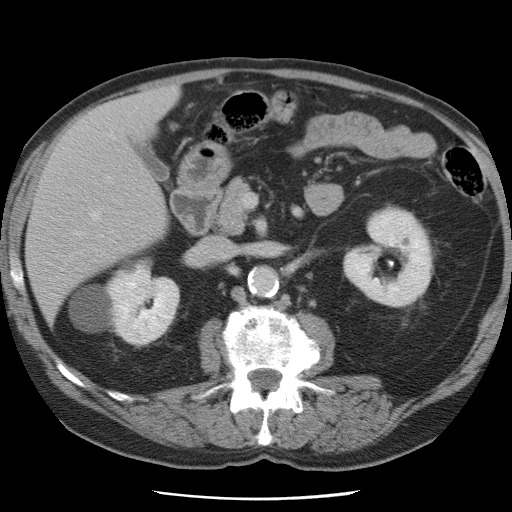
Contrast-enhanced abdominal CT, one axial slice. Position 34 of 78 along the scan axis. Intravenous contrast given. Soft-tissue window (W 400 / L 40 HU). 5 mm slice thickness. 512 × 512 image matrix. Male patient, age 75 years. Case-level facts recorded for this patient, not image findings: diagnosis: colorectal cancer liver metastases, imaged before liver resection; multiple liver metastases: yes; largest metastasis: 2.4 cm; disease in both lobes: yes.
Annotated regions visible in this slice (expert manual segmentation):
- hepatic veins: bounding box <74,137,113,236> (left, top, right, bottom; pixels)
- liver: <27,87,178,318>
- planned liver remnant (the part of the liver to remain after resection): <27,117,168,318>
- portal vein (with intrahepatic branches): <107,178,109,180>